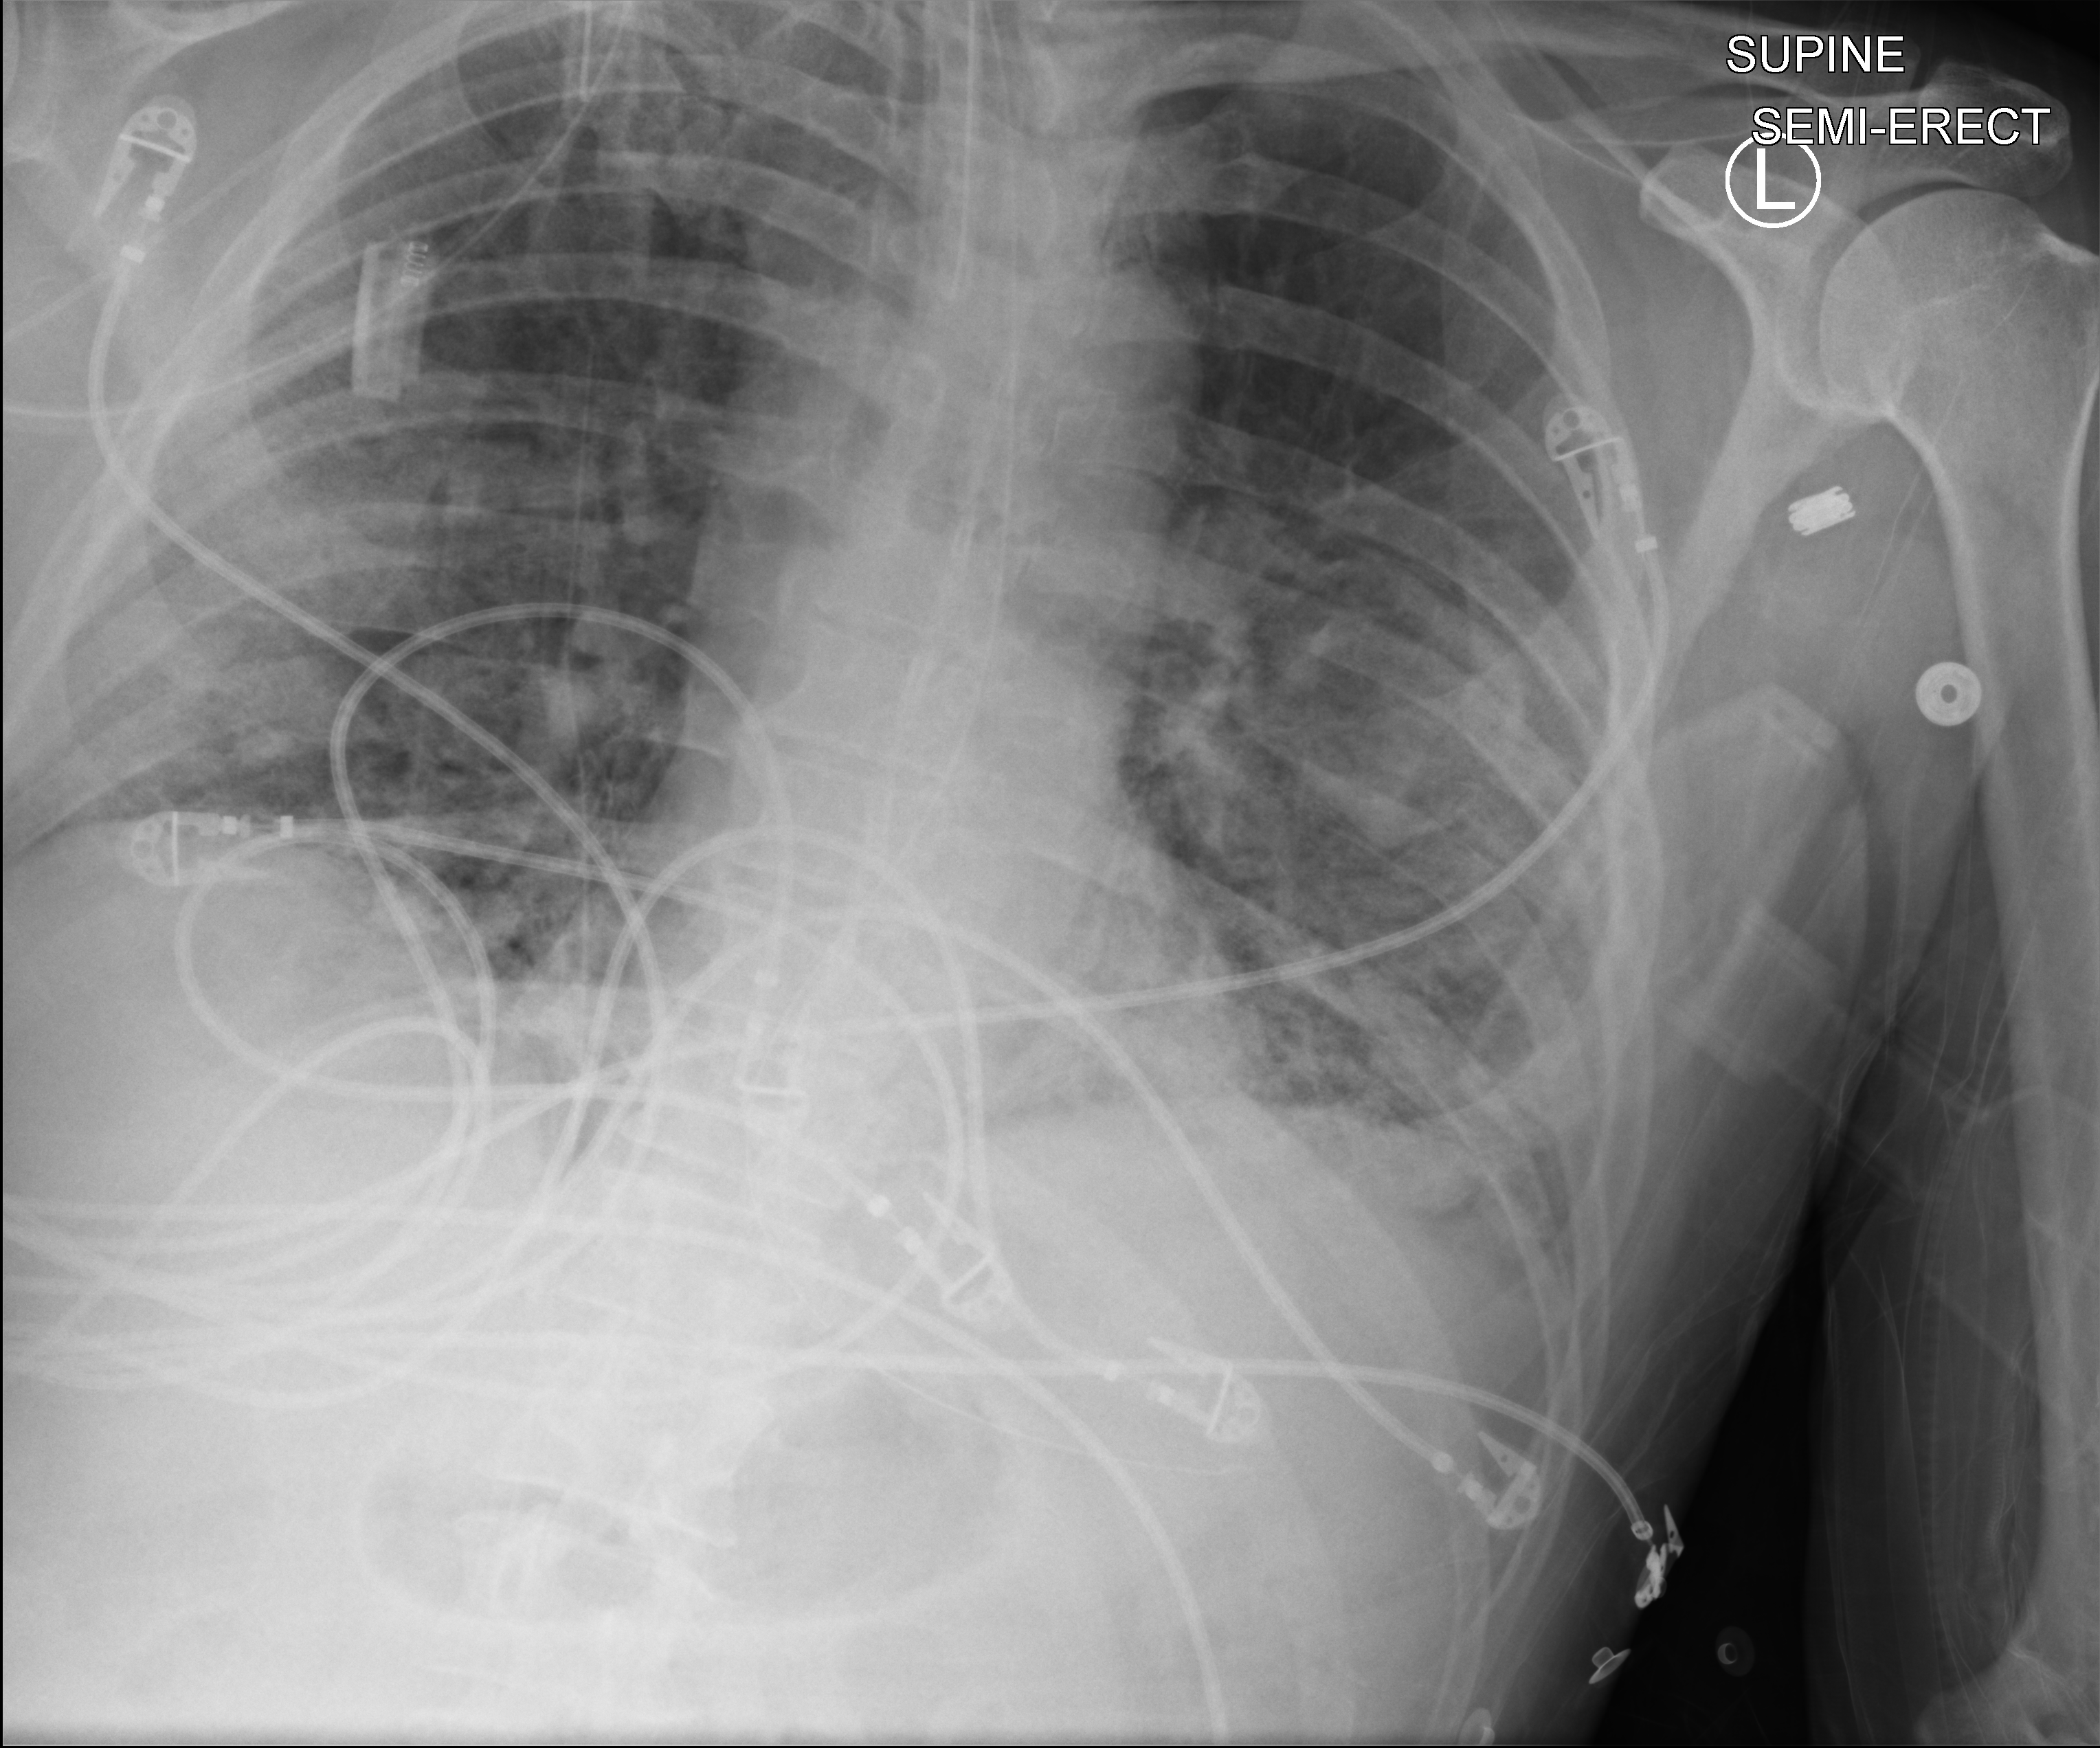
Chest X-ray (portable), anteroposterior (AP) projection. Male patient hospitalised with COVID-19, age 60–74 years.
Hospital-stay facts (about this admission, not read from this image; timing relative to this image not recorded):
- admitted to intensive care during this hospital stay: yes
- hypertension (admission record): no